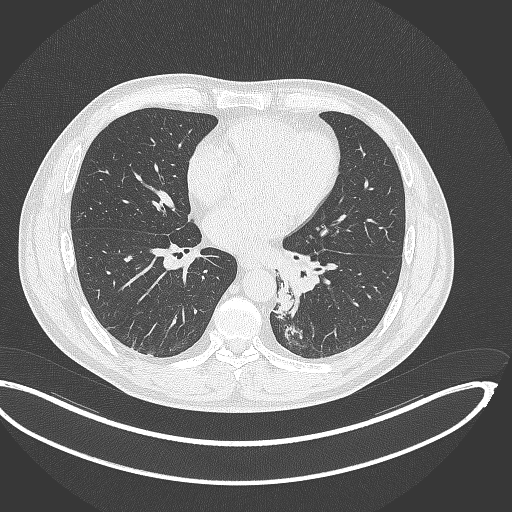
Chest CT, one axial slice. Lung window (W 1500 / L -600 HU). 1 mm slice thickness. 512 × 512 image matrix, field of view 442 × 442 mm. Male patient, age 50 years. From the clinical record (not read from this slice): clinical TNM (as recorded): T2a N3 M0.
Annotated regions visible in this slice (bounding box drawn by a radiologist):
- lung tumour (recorded histology: squamous cell carcinoma): bounding box [x1, y1, x2, y2] px = [271, 280, 296, 317]